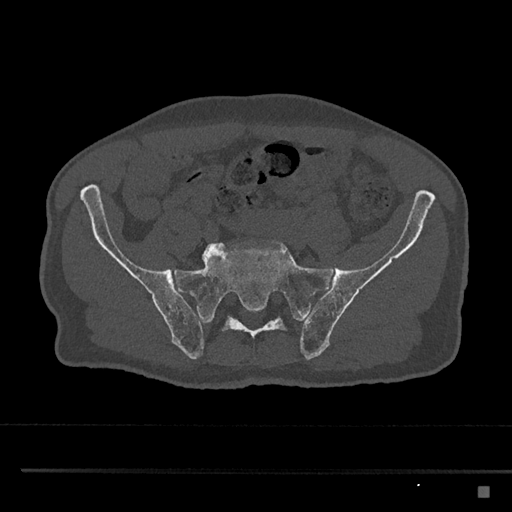
CT including the spine, one axial slice. Position 522 of 797 along the scan axis. Reconstruction kernel Br40s/3. 120 kVp. Bone window (W 1800 / L 400 HU). 0.5 mm slice thickness. 512 × 512 image matrix, field of view 391 × 391 mm. Patient: male, 59 years. Case-level facts recorded for this patient, not image findings: primary cancer: prostate.
Annotated regions visible in this slice (semi-automatic segmentation, software-assisted and operator-edited):
- L5 vertebra: bounding box [x1, y1, x2, y2] px = [202, 242, 267, 263]